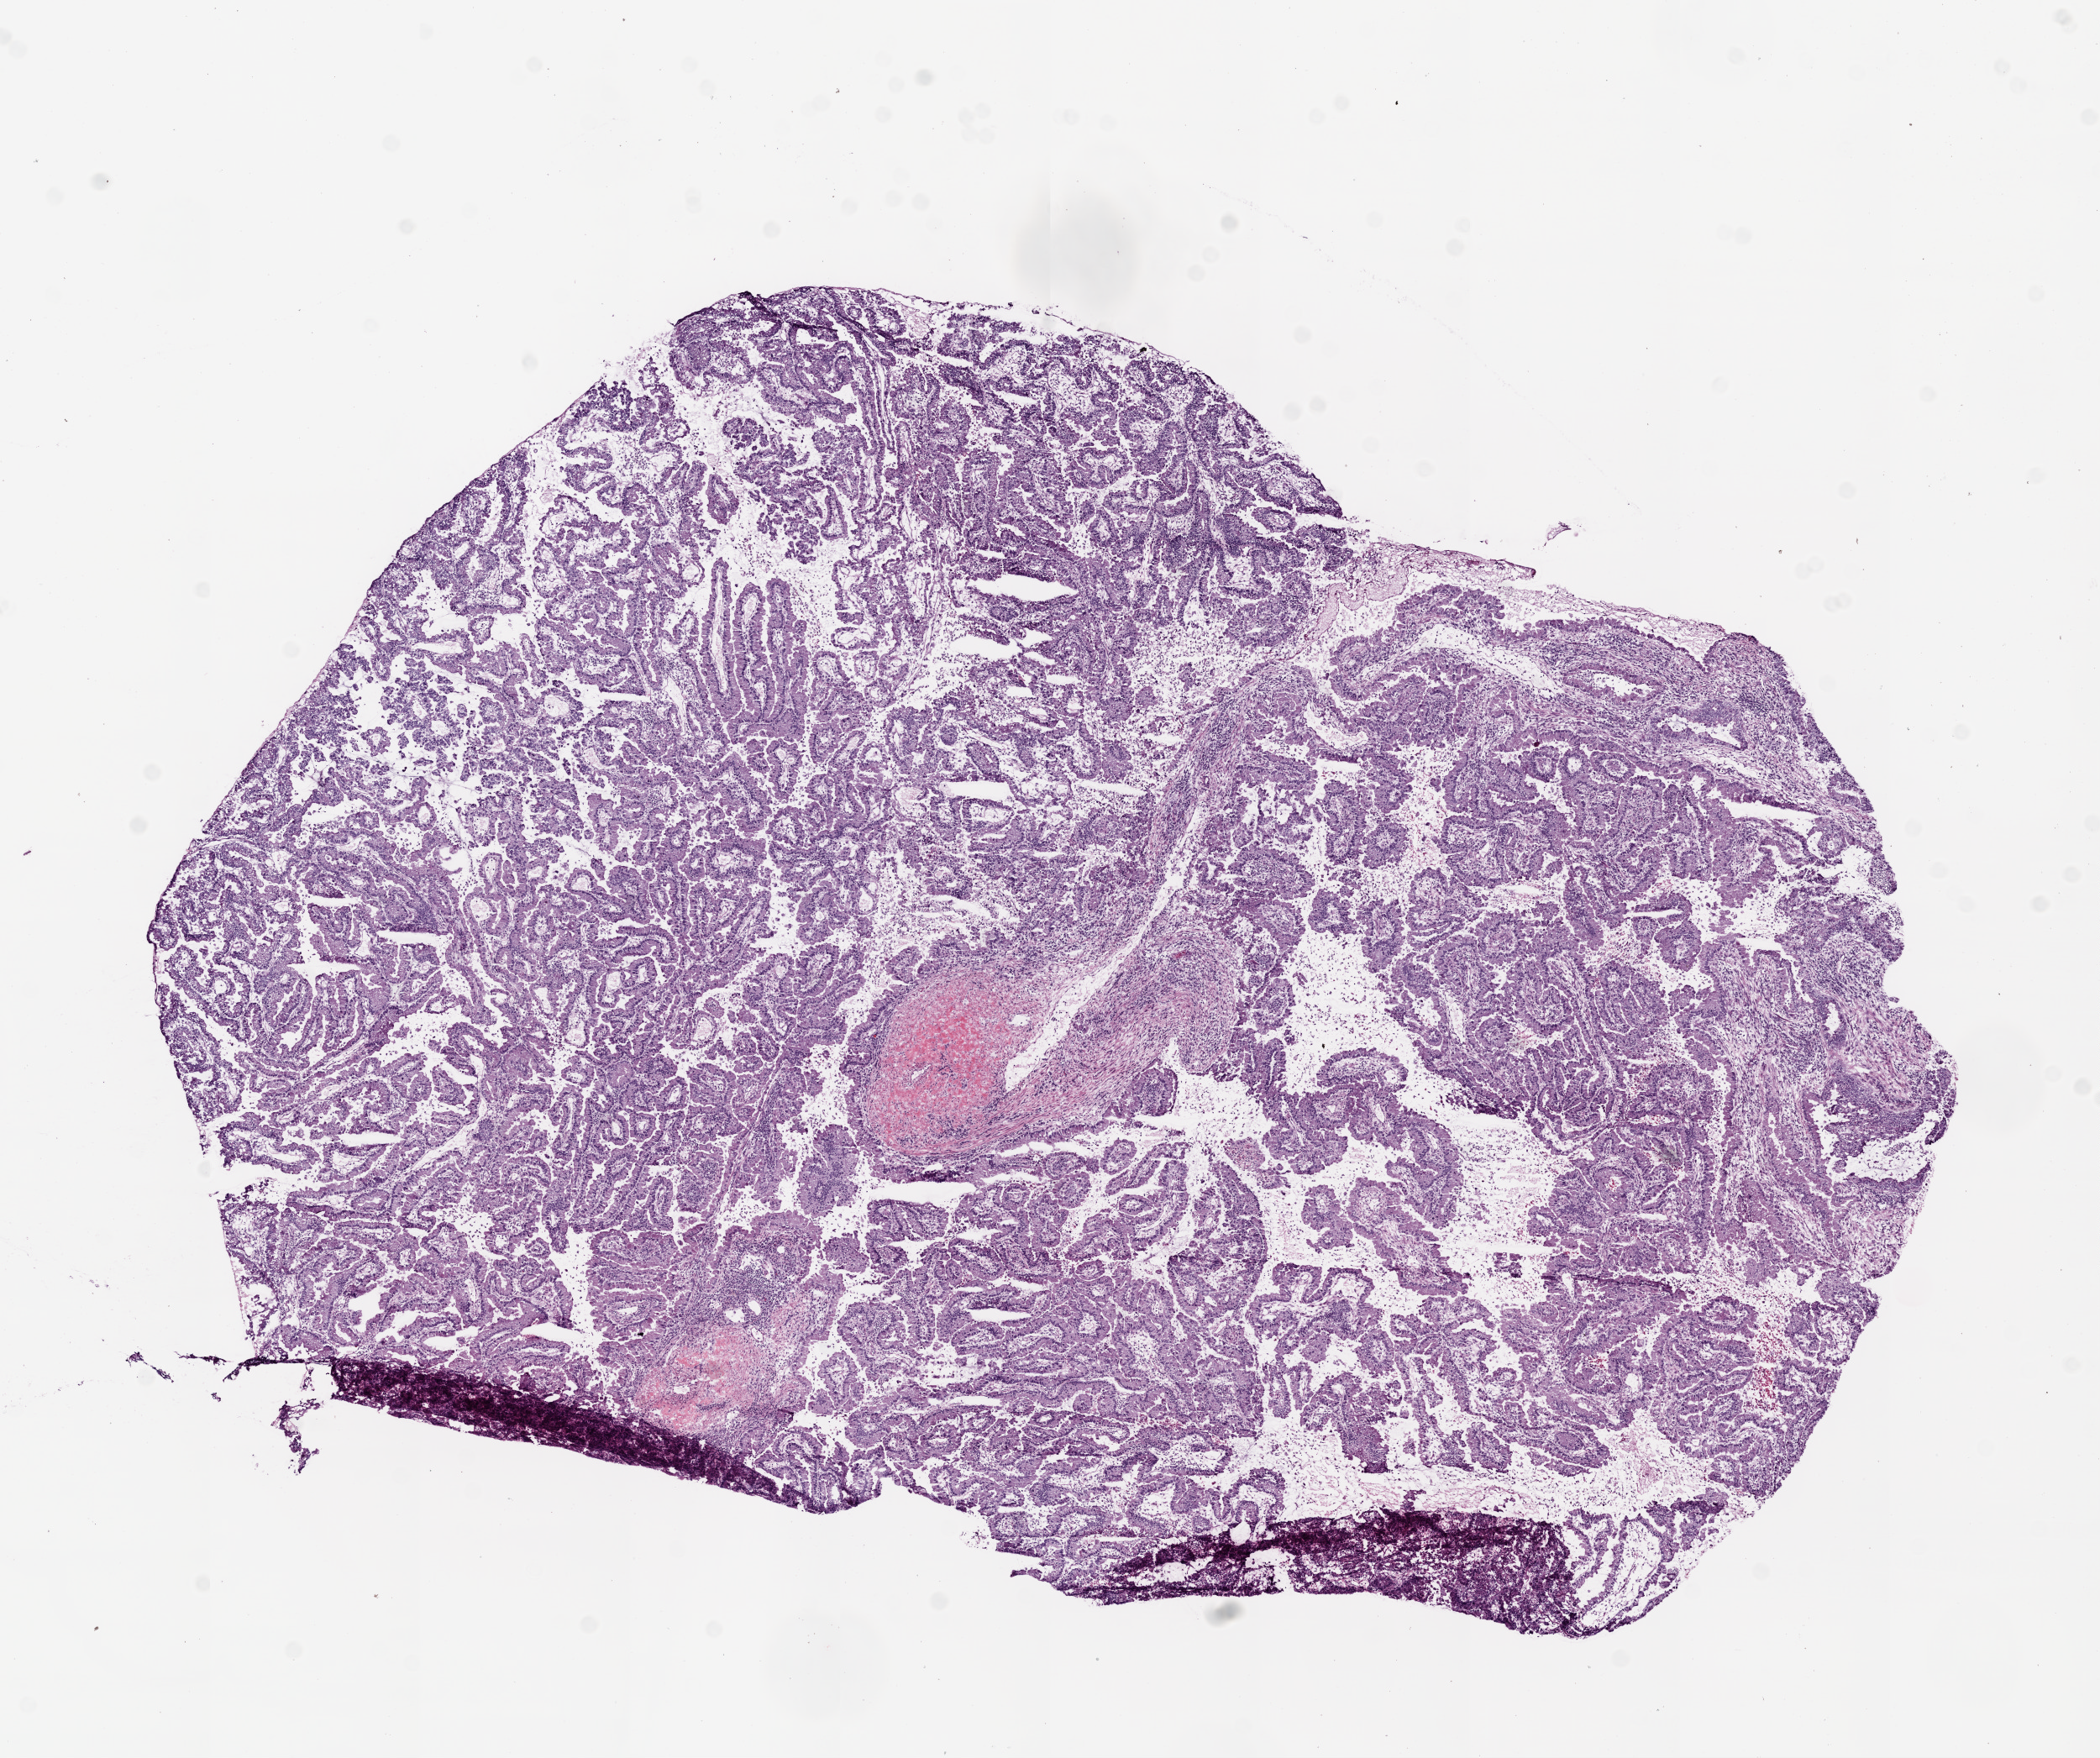
H&E-stained whole-slide image, low-resolution overview of the scanned area, about 10.0 x 8.4 mm (acquisition: 20x scan); frozen section from the bottom of the tissue portion; sample: primary tumour, lung. Male, age 41 years at initial diagnosis. Slide review estimates, as recorded: tumour cells 80%, tumour nuclei 75%, normal cells 0%, stromal cells 20%, necrosis 0%.
AJCC pathologic stage: IB (6th edition). Laterality: right. Diagnosis: Adenocarcinoma with mixed subtypes (lower lobe, lung).